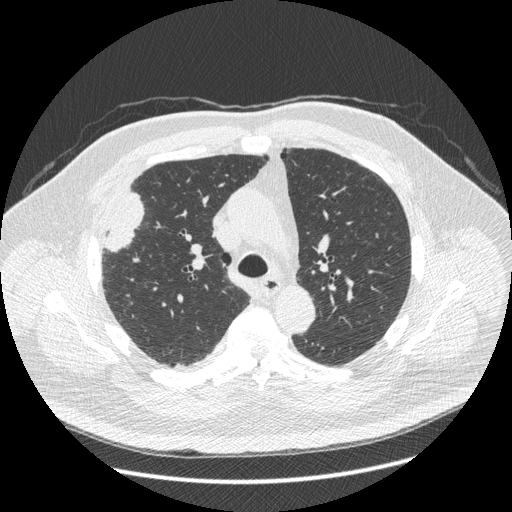
Axial slice from a low-dose chest CT screening exam; third screening round (two years after baseline); lung window (W 1500 / L -600 HU); 1.25 mm slice thickness; standard (soft-tissue) reconstruction kernel (STANDARD); slice 134 of 426 in the series; 512 × 512 image matrix, field of view 400 × 400 mm. Male participant, aged 66 years at enrolment. Current smoker at enrolment.
- Lesion marked by an expert reader, box from (x=87, y=194) to (x=146, y=267) px.
- The exam's reader record, not a measurement of the box and not confirmed to be the same lesion: non-calcified nodule or mass ≥4 mm, right upper lobe, 48 × 25 mm, spiculated (stellate) margins, soft tissue attenuation, pre-existing on the prior screen: no.
- Official screen result: positive, other.